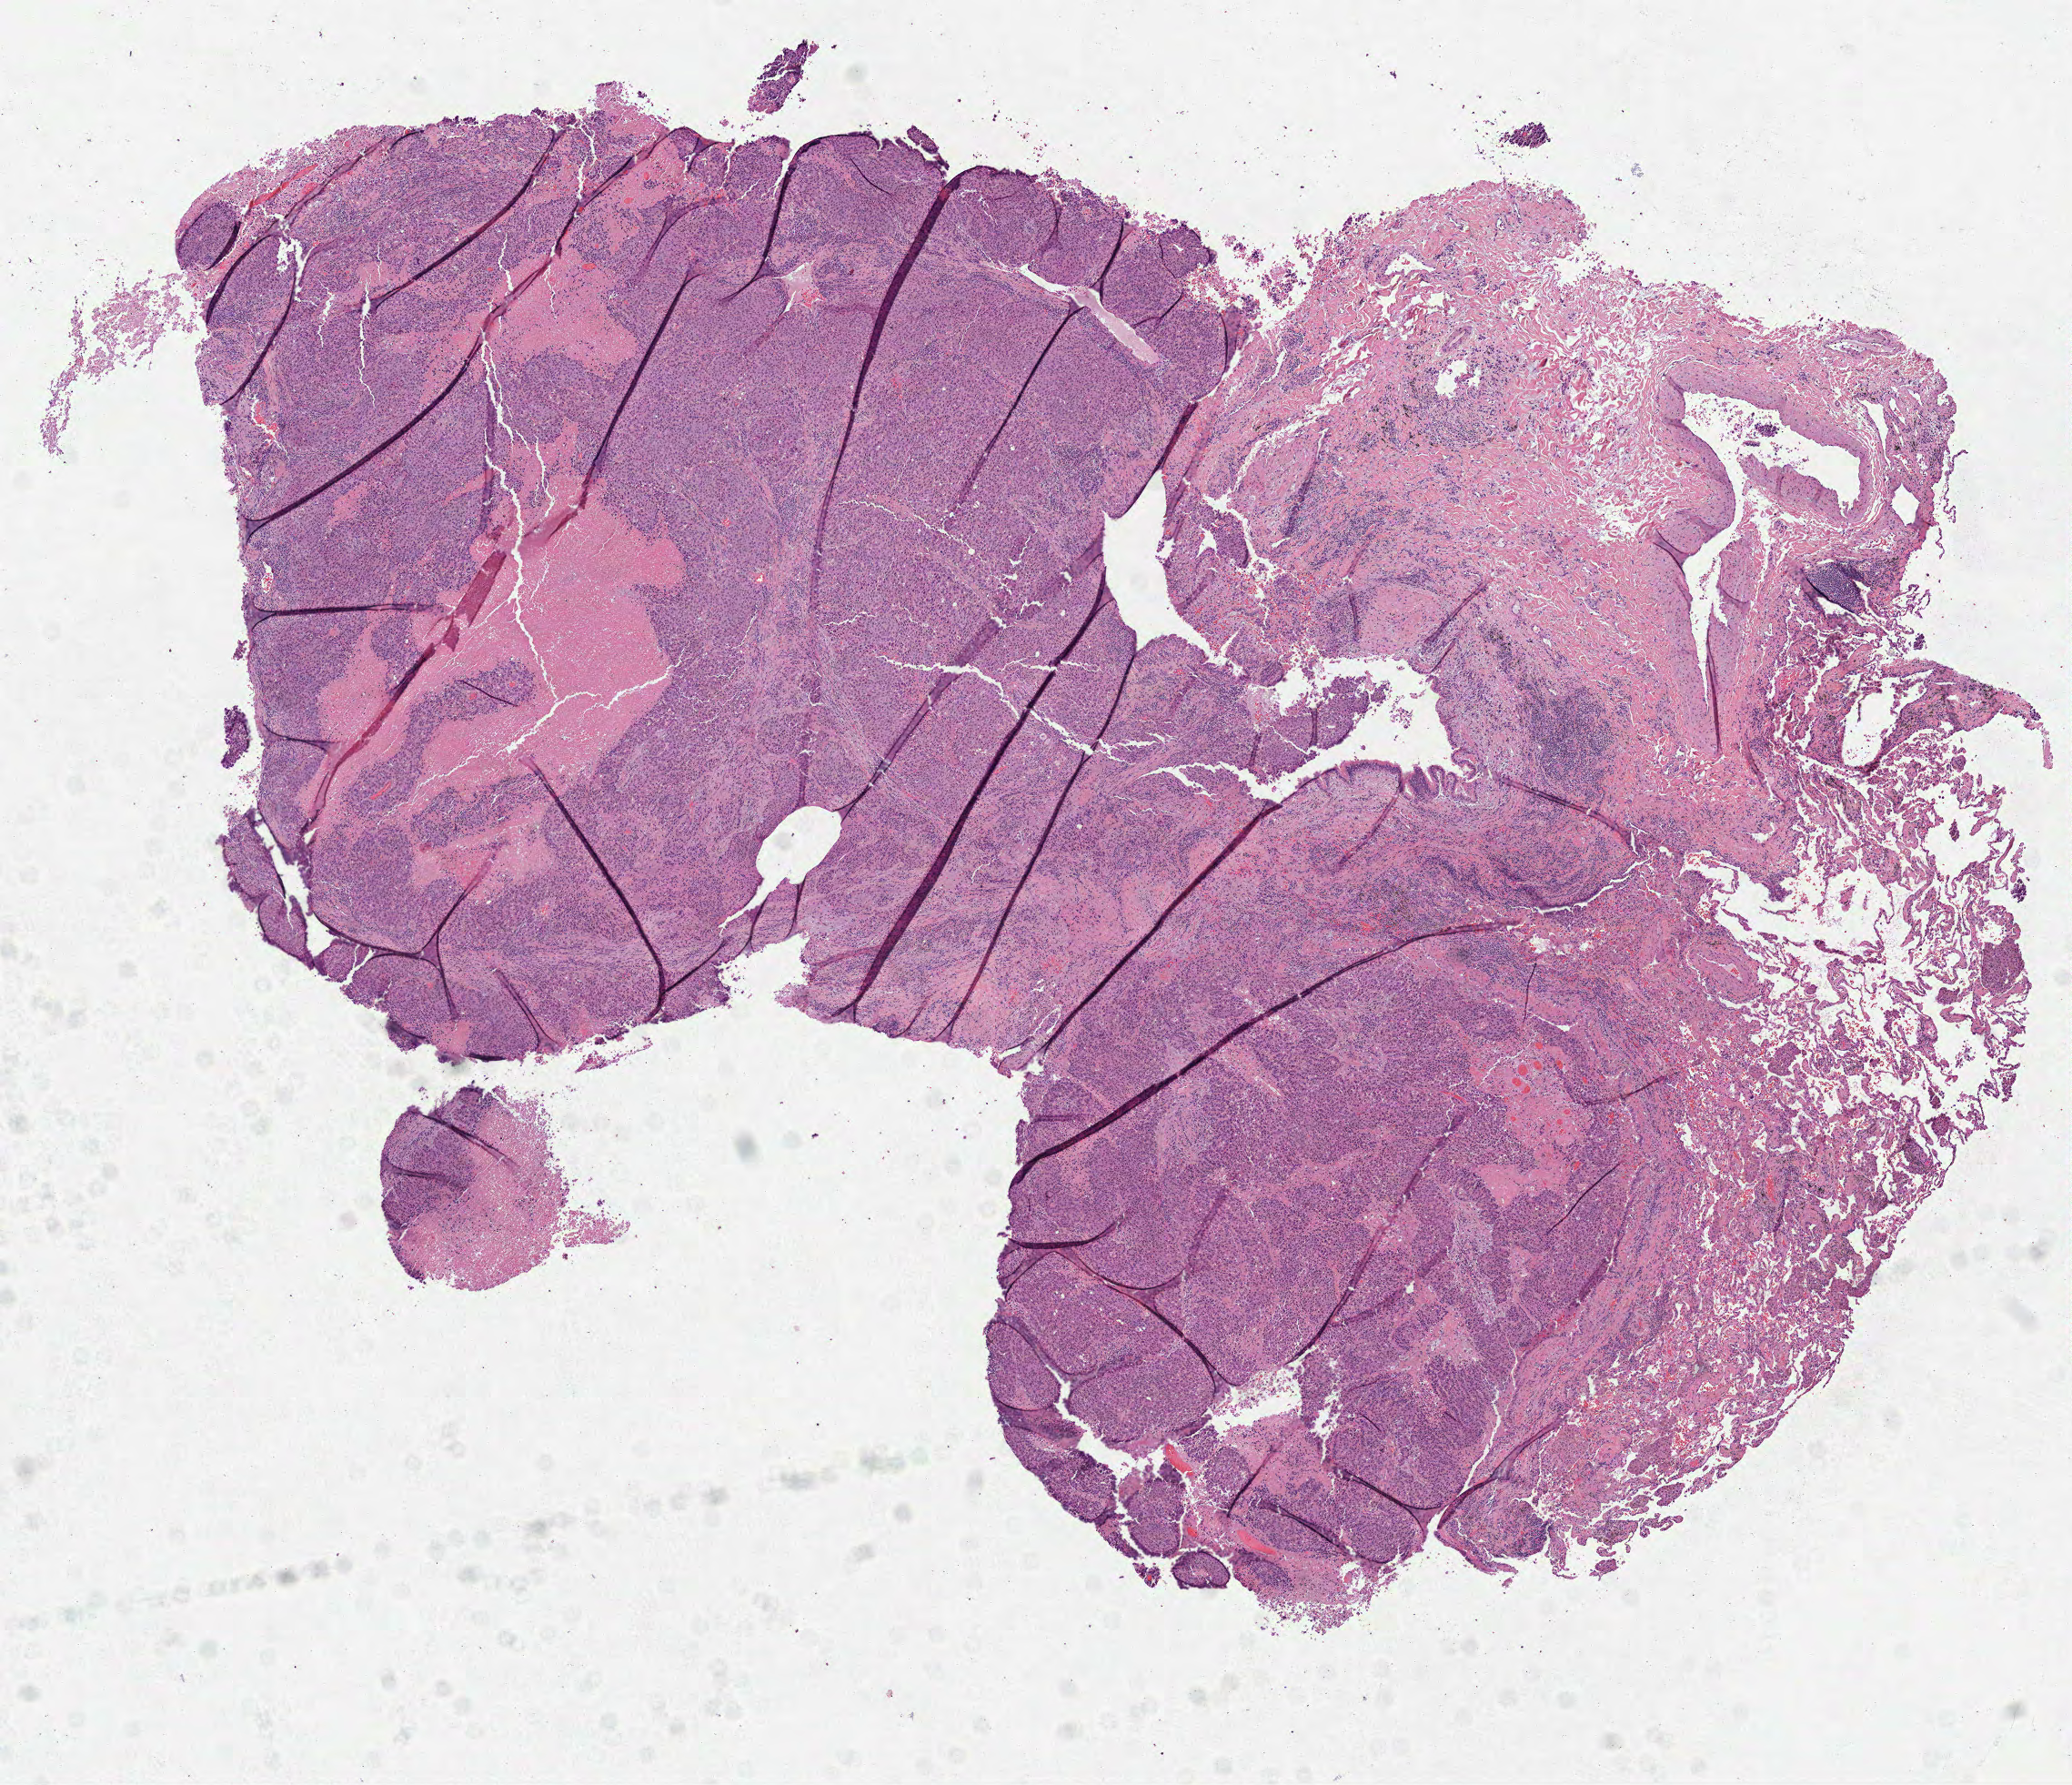
Whole-slide histology image, H&E, shown as a low-resolution overview of the whole scanned area (about 9.2 x 7.9 mm, from a 40x scan); formalin-fixed paraffin-embedded (FFPE) diagnostic section; lung, primary tumour sample. Male patient; age at initial diagnosis 58 years.
Laterality: right. Histologic diagnosis: Adenocarcinoma, NOS (upper lobe, lung).